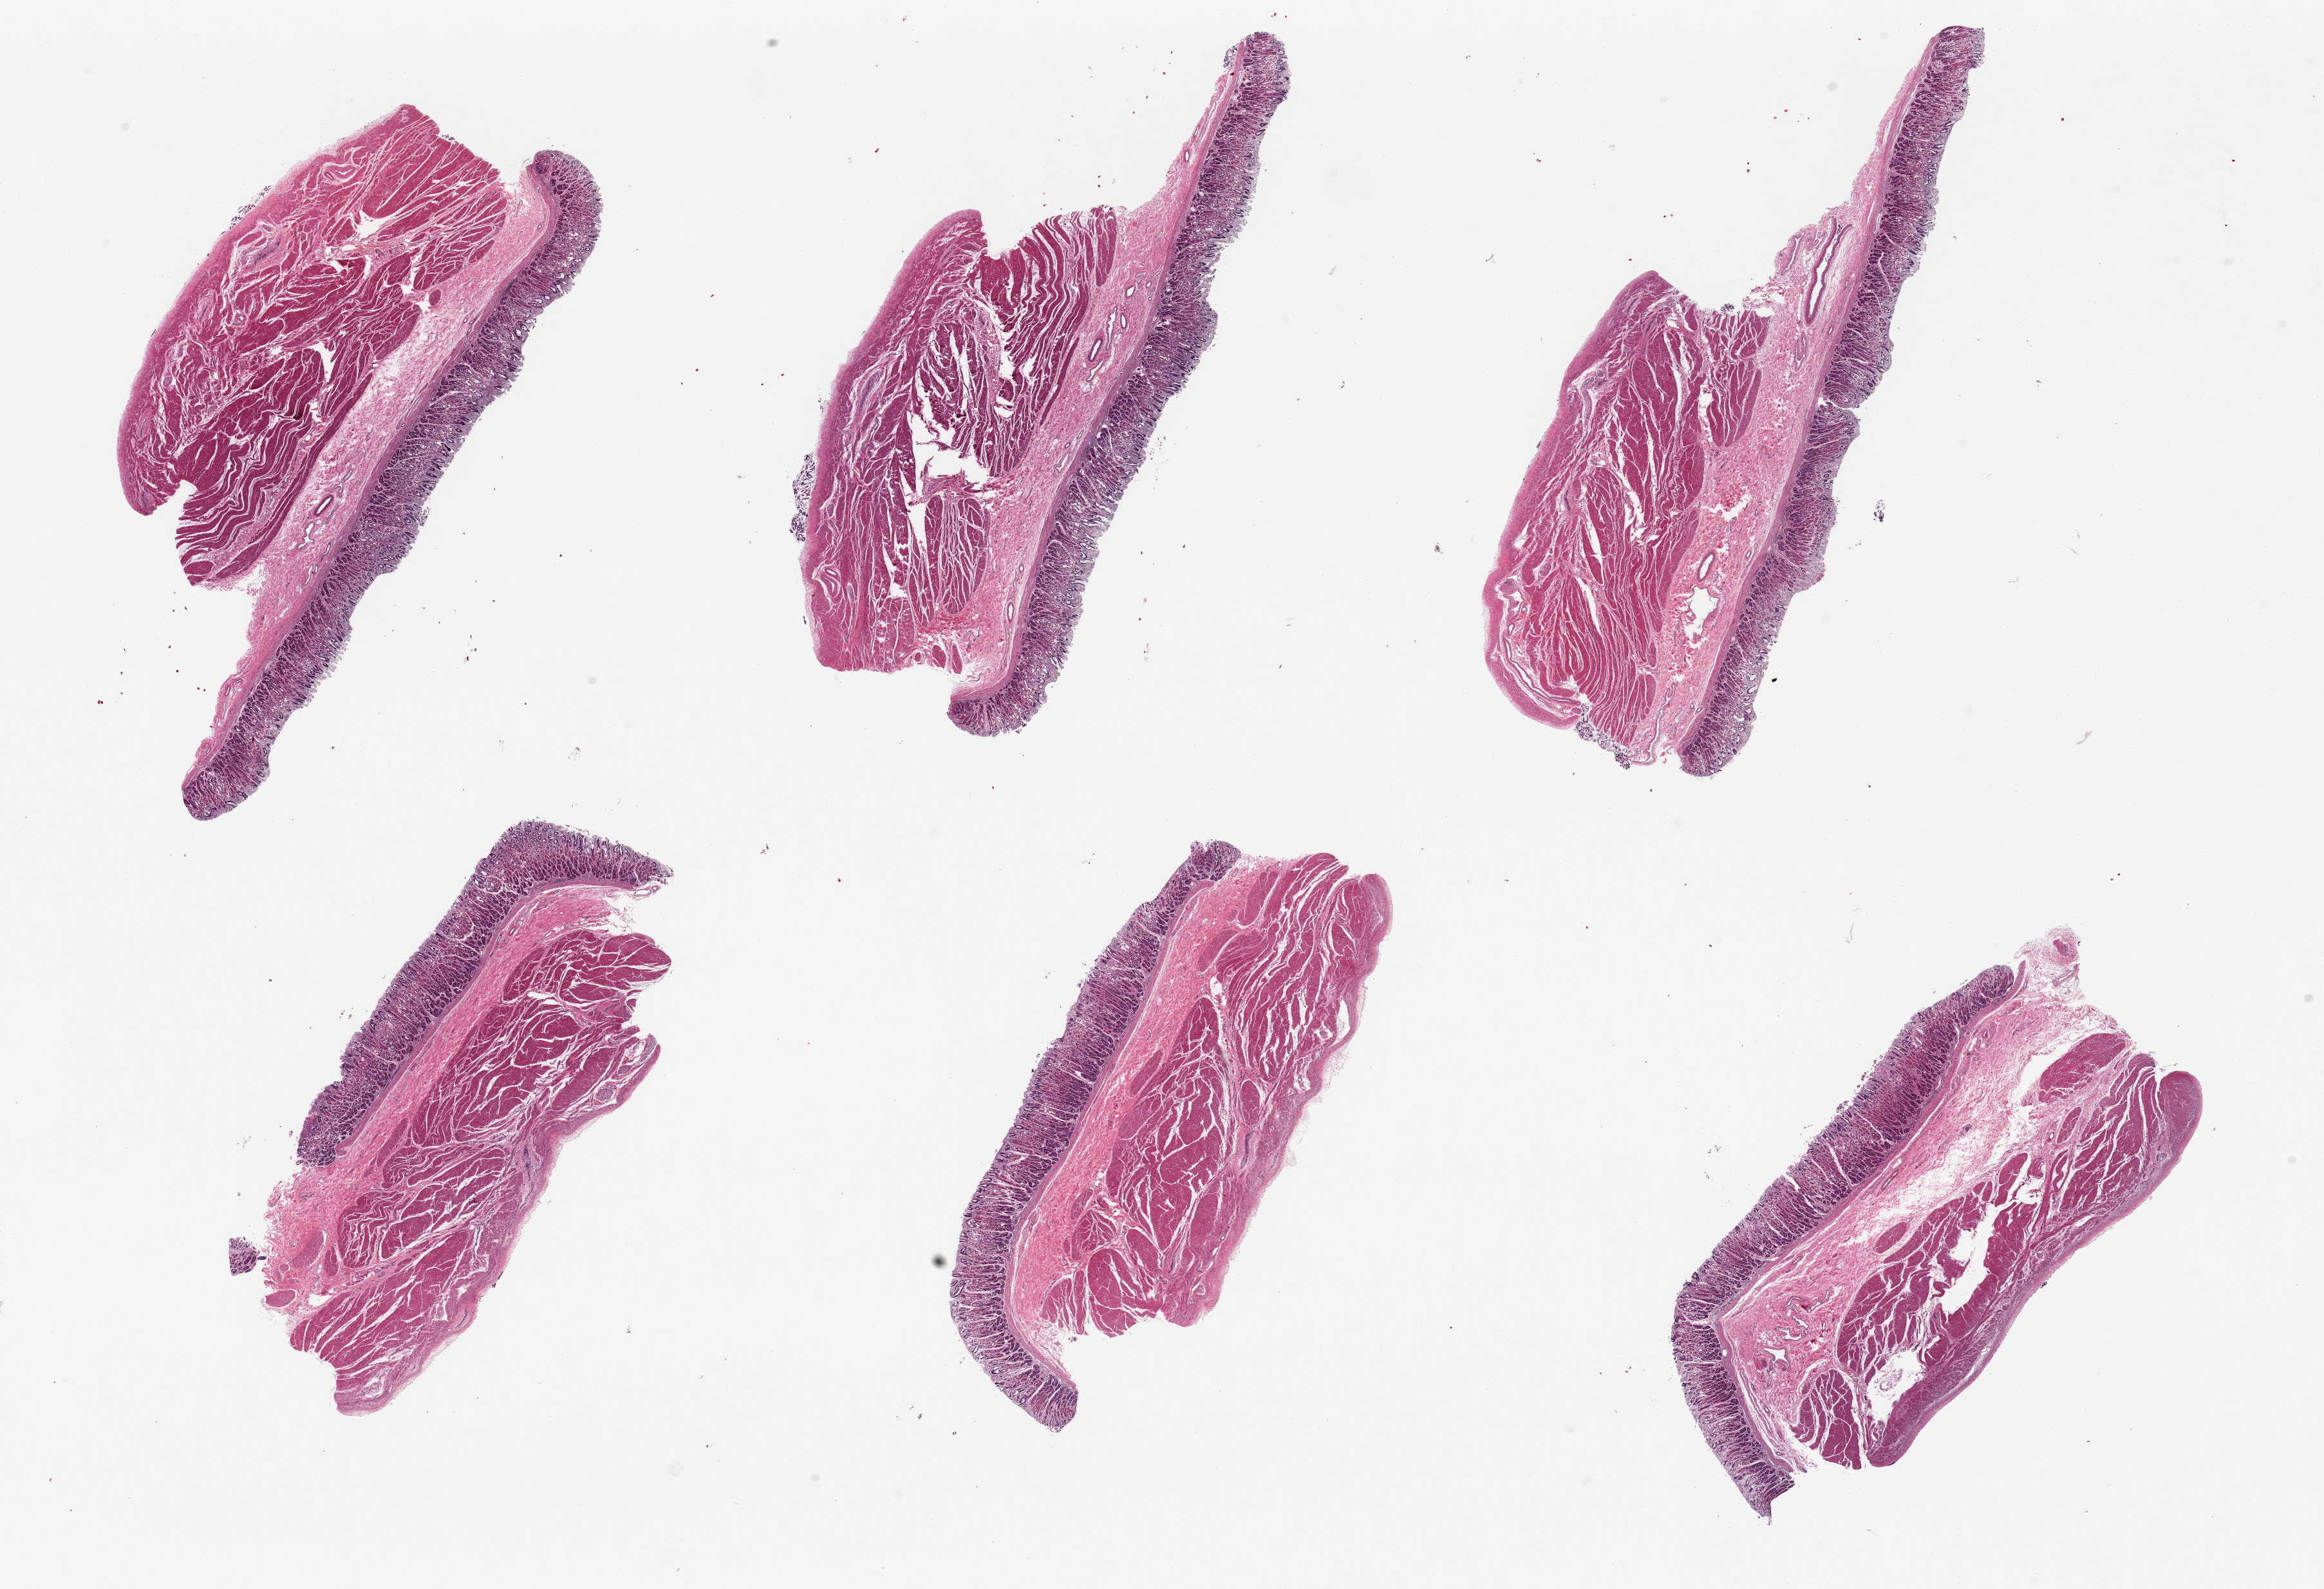
H&E whole-slide image, a low-resolution overview of the entire scanned area, about 28.5 x 19.5 mm. PAXgene-fixed, paraffin-embedded tissue. Section of stomach (target tissue). Donor tissue sample. Male donor.
Reviewer comment on this tissue sample: 6 pieces; all are stomach mucosa and muscularis (not colon).